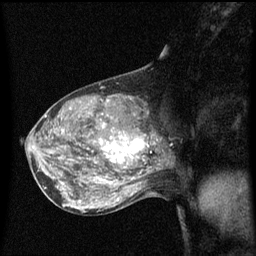
Breast MRI (dynamic contrast-enhanced), one sagittal slice. Slice 32 of 60 in the series (ordered by position). Dynamic contrast-enhanced series, image 2 of 3 at this slice position (ordered by acquisition). 1.5 T. TE 4.2 ms, TR 8.4 ms. 2 mm slice thickness. 256 × 256 image matrix, field of view 200 × 200 mm. Patient: female, 50 years.
Outlined on this slice (semi-automatic segmentation, software-assisted and operator-edited):
- analysis volume of interest (the breast-tissue region the enhancement analysis was run in; not a lesion): bounding box (x1, y1, x2, y2) in pixels: (100, 114, 153, 171)
- tumour enhancement mask (voxels above the 70 % enhancement threshold inside the analysis volume of interest): (100, 134, 148, 163)